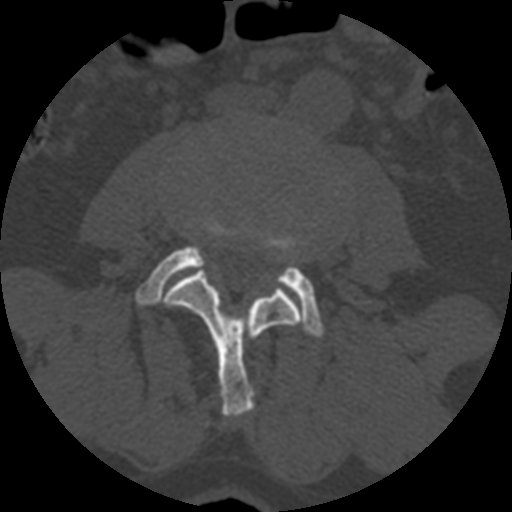
CT including the spine, one axial slice. Position 295 of 399 along the scan axis. 120 kVp. Bone window (W 1800 / L 400 HU). 1.25 mm slice thickness. 512 × 512 image matrix, field of view 160 × 160 mm. Patient age 71 years. Case-level facts recorded for this patient, not image findings: primary cancer: prostate.
Outlined on this slice (semi-automatic segmentation, software-assisted and operator-edited):
- L3 vertebra: box from (x=164, y=267) to (x=302, y=417) px
- L4 vertebra: (x=136, y=216)–(x=323, y=339)